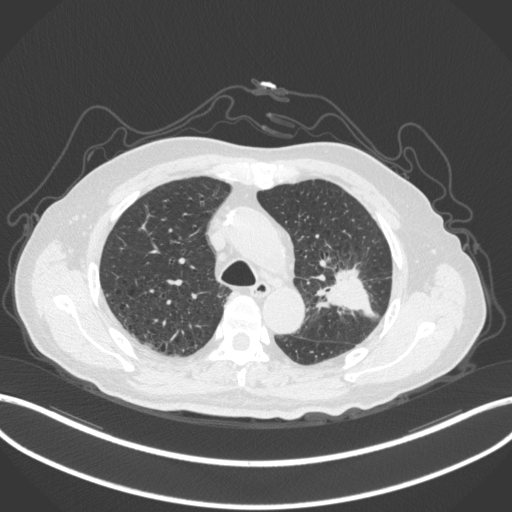
Chest CT, one axial slice; slice 204 of 331 in the series (ordered by position); reconstruction kernel B31f; lung window (W 1500 / L -600 HU); 512 × 512 image matrix. Male patient, age 79 years. Case-level facts recorded for this patient, not image findings: clinical TNM (as recorded): T2a N1 M1; histopathological grade: G3.
Annotated regions visible in this slice (bounding box drawn by a radiologist):
- lung tumour (recorded histology: adenocarcinoma): bounding box (x1, y1, x2, y2) in pixels: (315, 261, 388, 327)